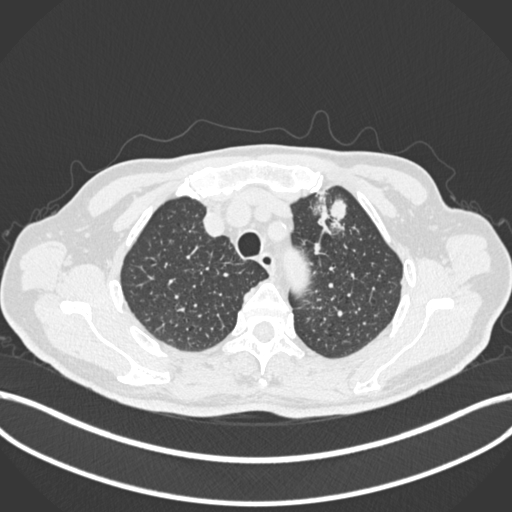
Chest CT, one axial slice. Position 209 of 261 along the scan axis. Reconstruction kernel B30f. Lung window (W 1500 / L -600 HU). 1 mm slice thickness. 512 × 512 image matrix, field of view 400 × 400 mm. Male patient, age 74 years. Case-level facts recorded for this patient, not image findings: clinical TNM (as recorded): T2b N0 M1c.
Annotated regions visible in this slice (bounding box drawn by a radiologist):
- lung tumour (recorded histology: adenocarcinoma): bounding box (x1, y1, x2, y2) in pixels: (312, 191, 356, 236)